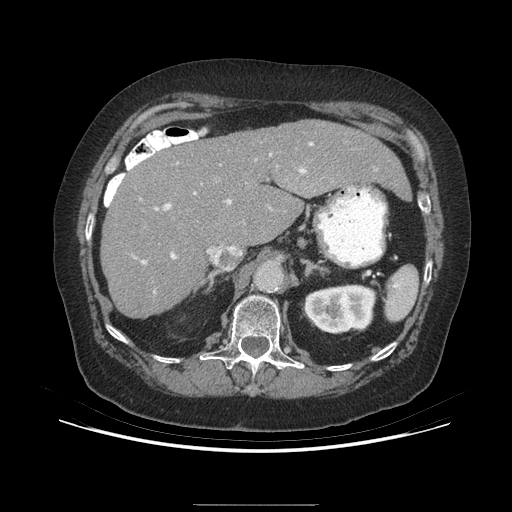
Contrast-enhanced abdominal CT (liver protocol), one axial slice; position 159 of 192 along the scan axis; 140 kVp; soft-tissue window (W 400 / L 40 HU); 2.5 mm slice thickness; 512 × 512 image matrix, field of view 400 × 400 mm. Case-level facts recorded for this patient, not image findings: diagnosis: hepatocellular carcinoma (patient treated with transarterial chemoembolisation; whether this scan precedes or follows treatment is not stated here); TNM stage (as recorded): Stage-I; Child-Pugh class: A; tumour size: 3.2 cm.
Structures marked on this image (semi-automatically segmented with operator editing):
- liver parenchyma outside the tumour (the mass and vessels are separate outlines, so this box may not span the whole liver): bounding box <100,120,406,316> (left, top, right, bottom; pixels)
- liver vessels: <134,142,313,293>